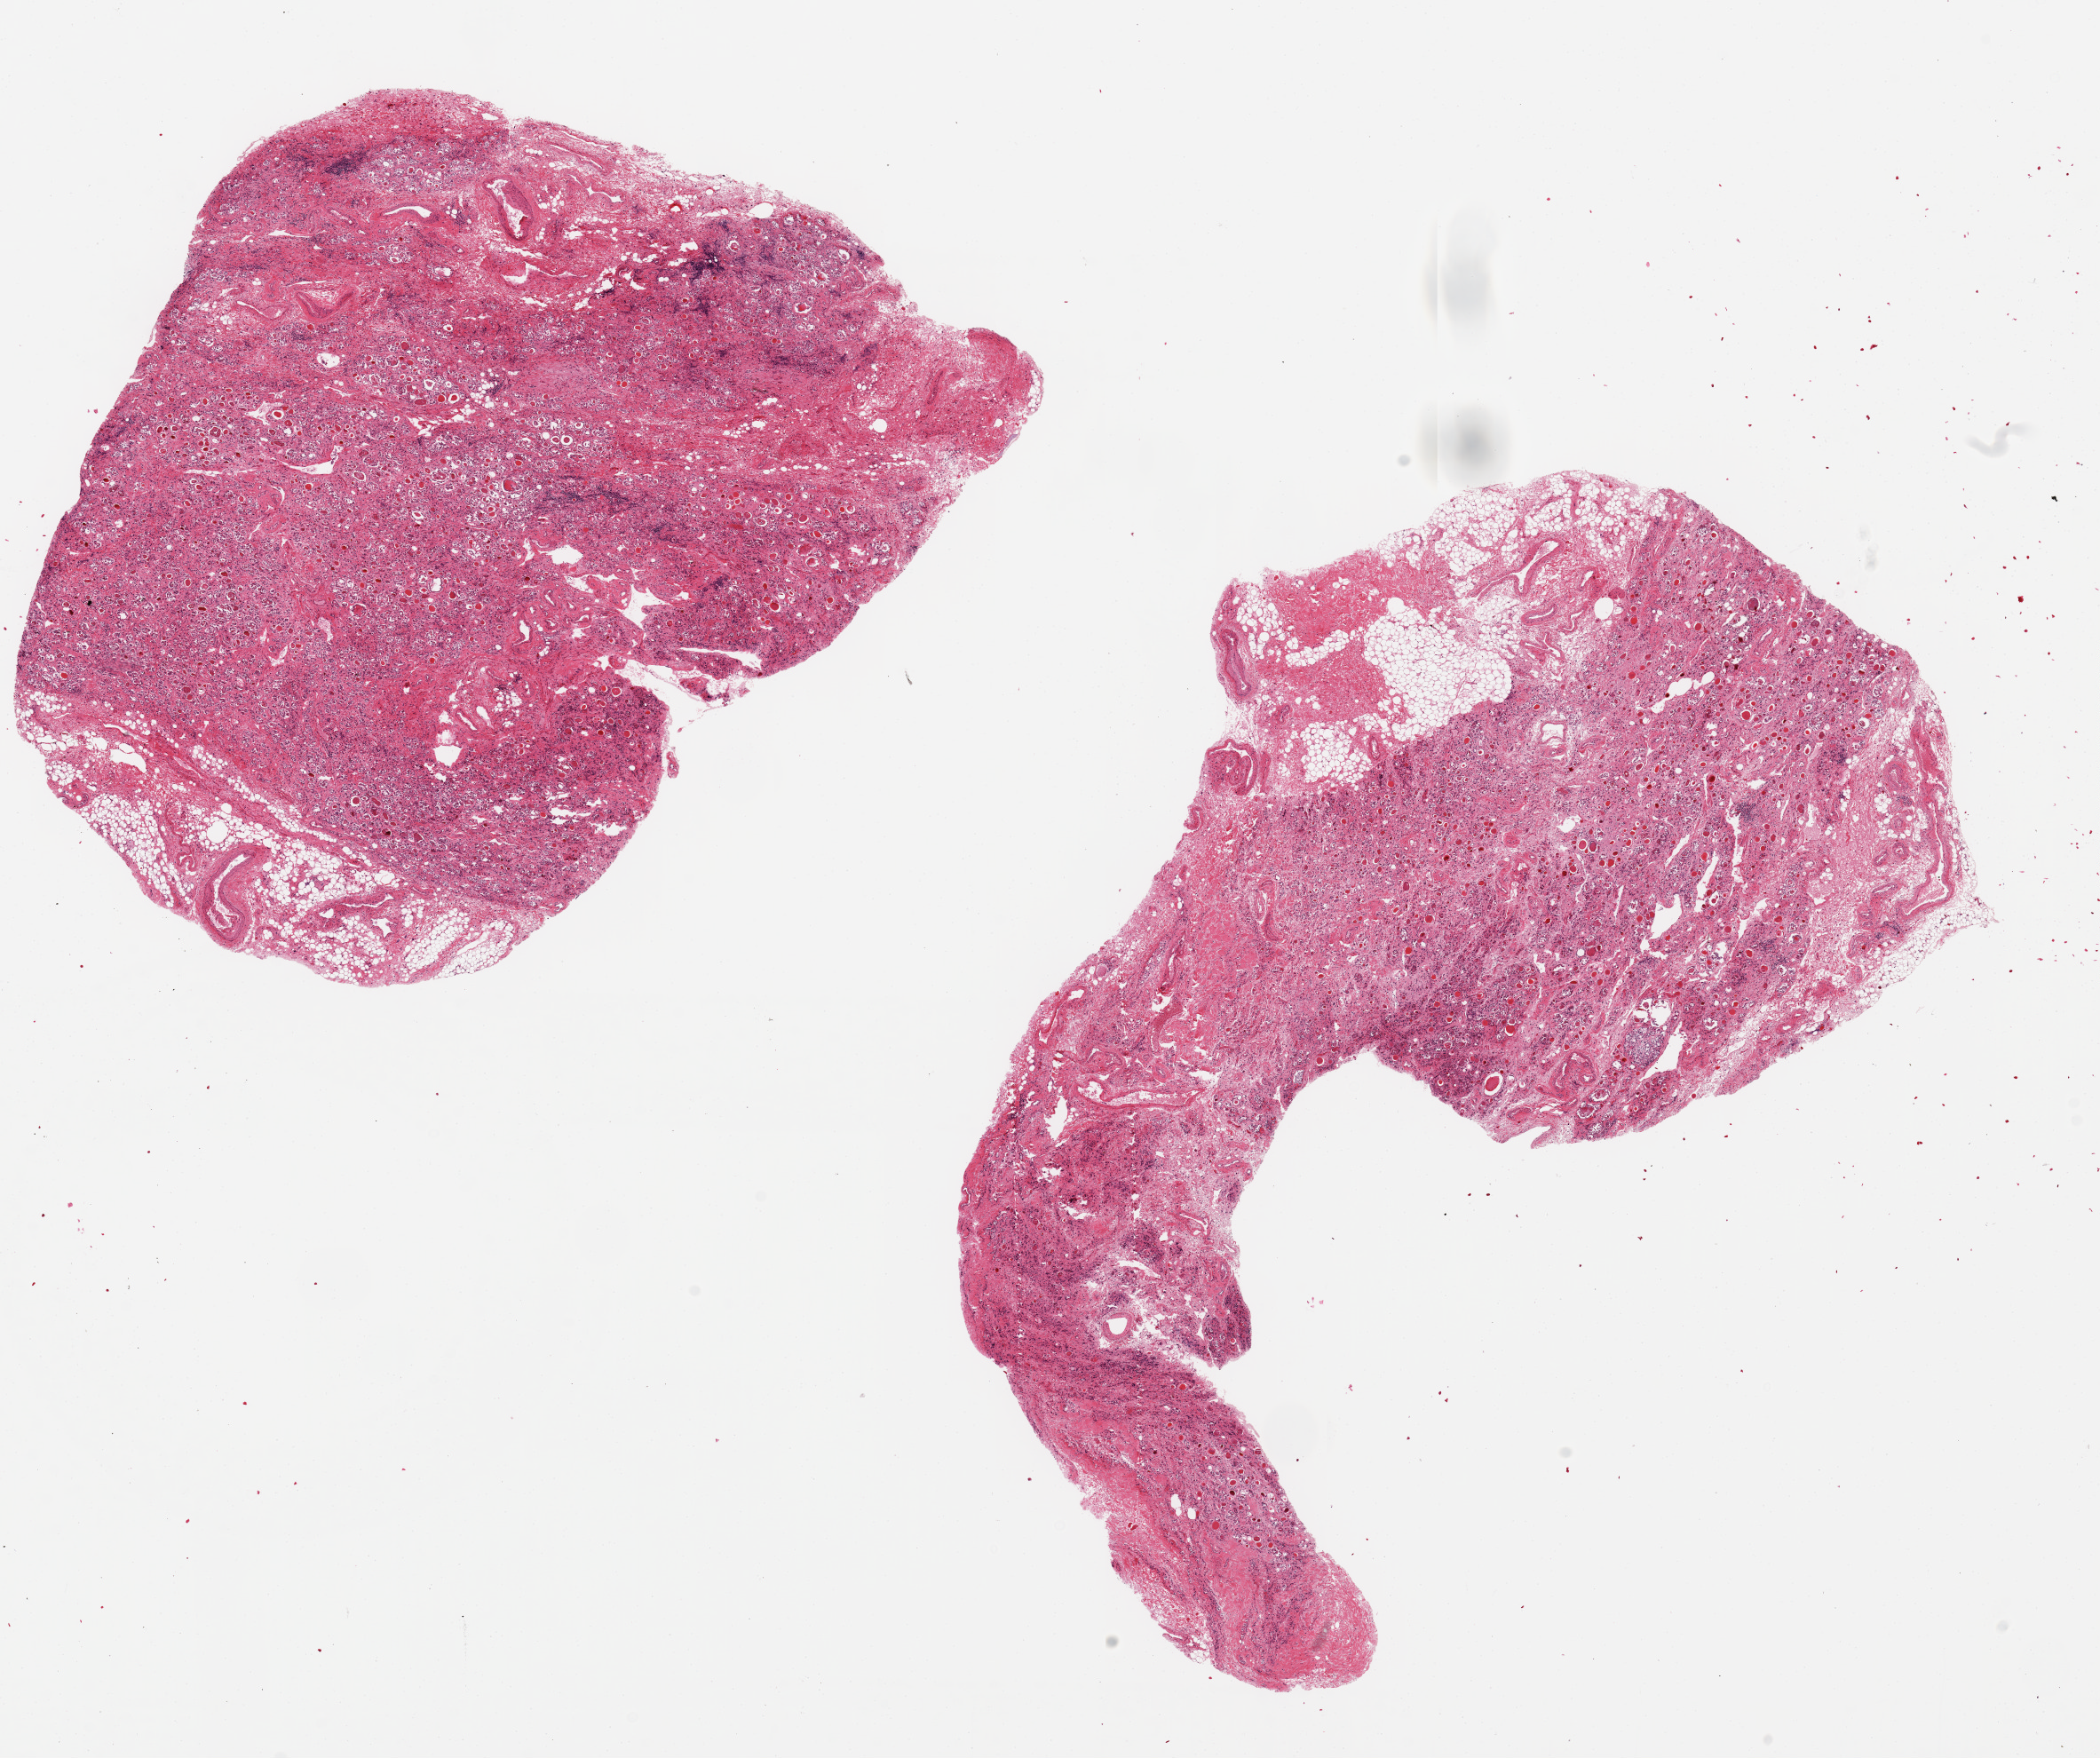
Whole-slide image, hematoxylin and eosin (H&E) stain, brightfield, shown as a low-resolution overview of the whole scanned area (about 18.7 x 15.7 mm); PAXgene-fixed paraffin-embedded (PFPE) section; sampled site (target tissue): thyroid; donor tissue sample. Female donor.
Review note (as recorded): 2 ~8x7mm aliquots. Suspect malignancy, ?follicular variant of papillary carcinoma, pending glass review. Autolysis hampers analysis.